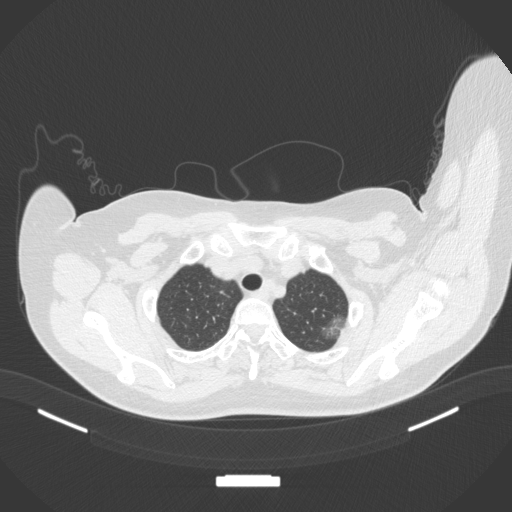
Chest CT, one axial slice. Position 322 of 386 along the scan axis. Reconstruction kernel B31f. Lung window (W 1500 / L -600 HU). 1 mm slice thickness. 512 × 512 image matrix, field of view 400 × 400 mm. Female patient, age 58 years. Case-level facts recorded for this patient, not image findings: clinical TNM (as recorded): T1c N0 M0.
Structures marked on this image (rectangle marked by the reading radiologist):
- lung tumour (recorded histology: adenocarcinoma): bounding box <320,311,351,341> (left, top, right, bottom; pixels)